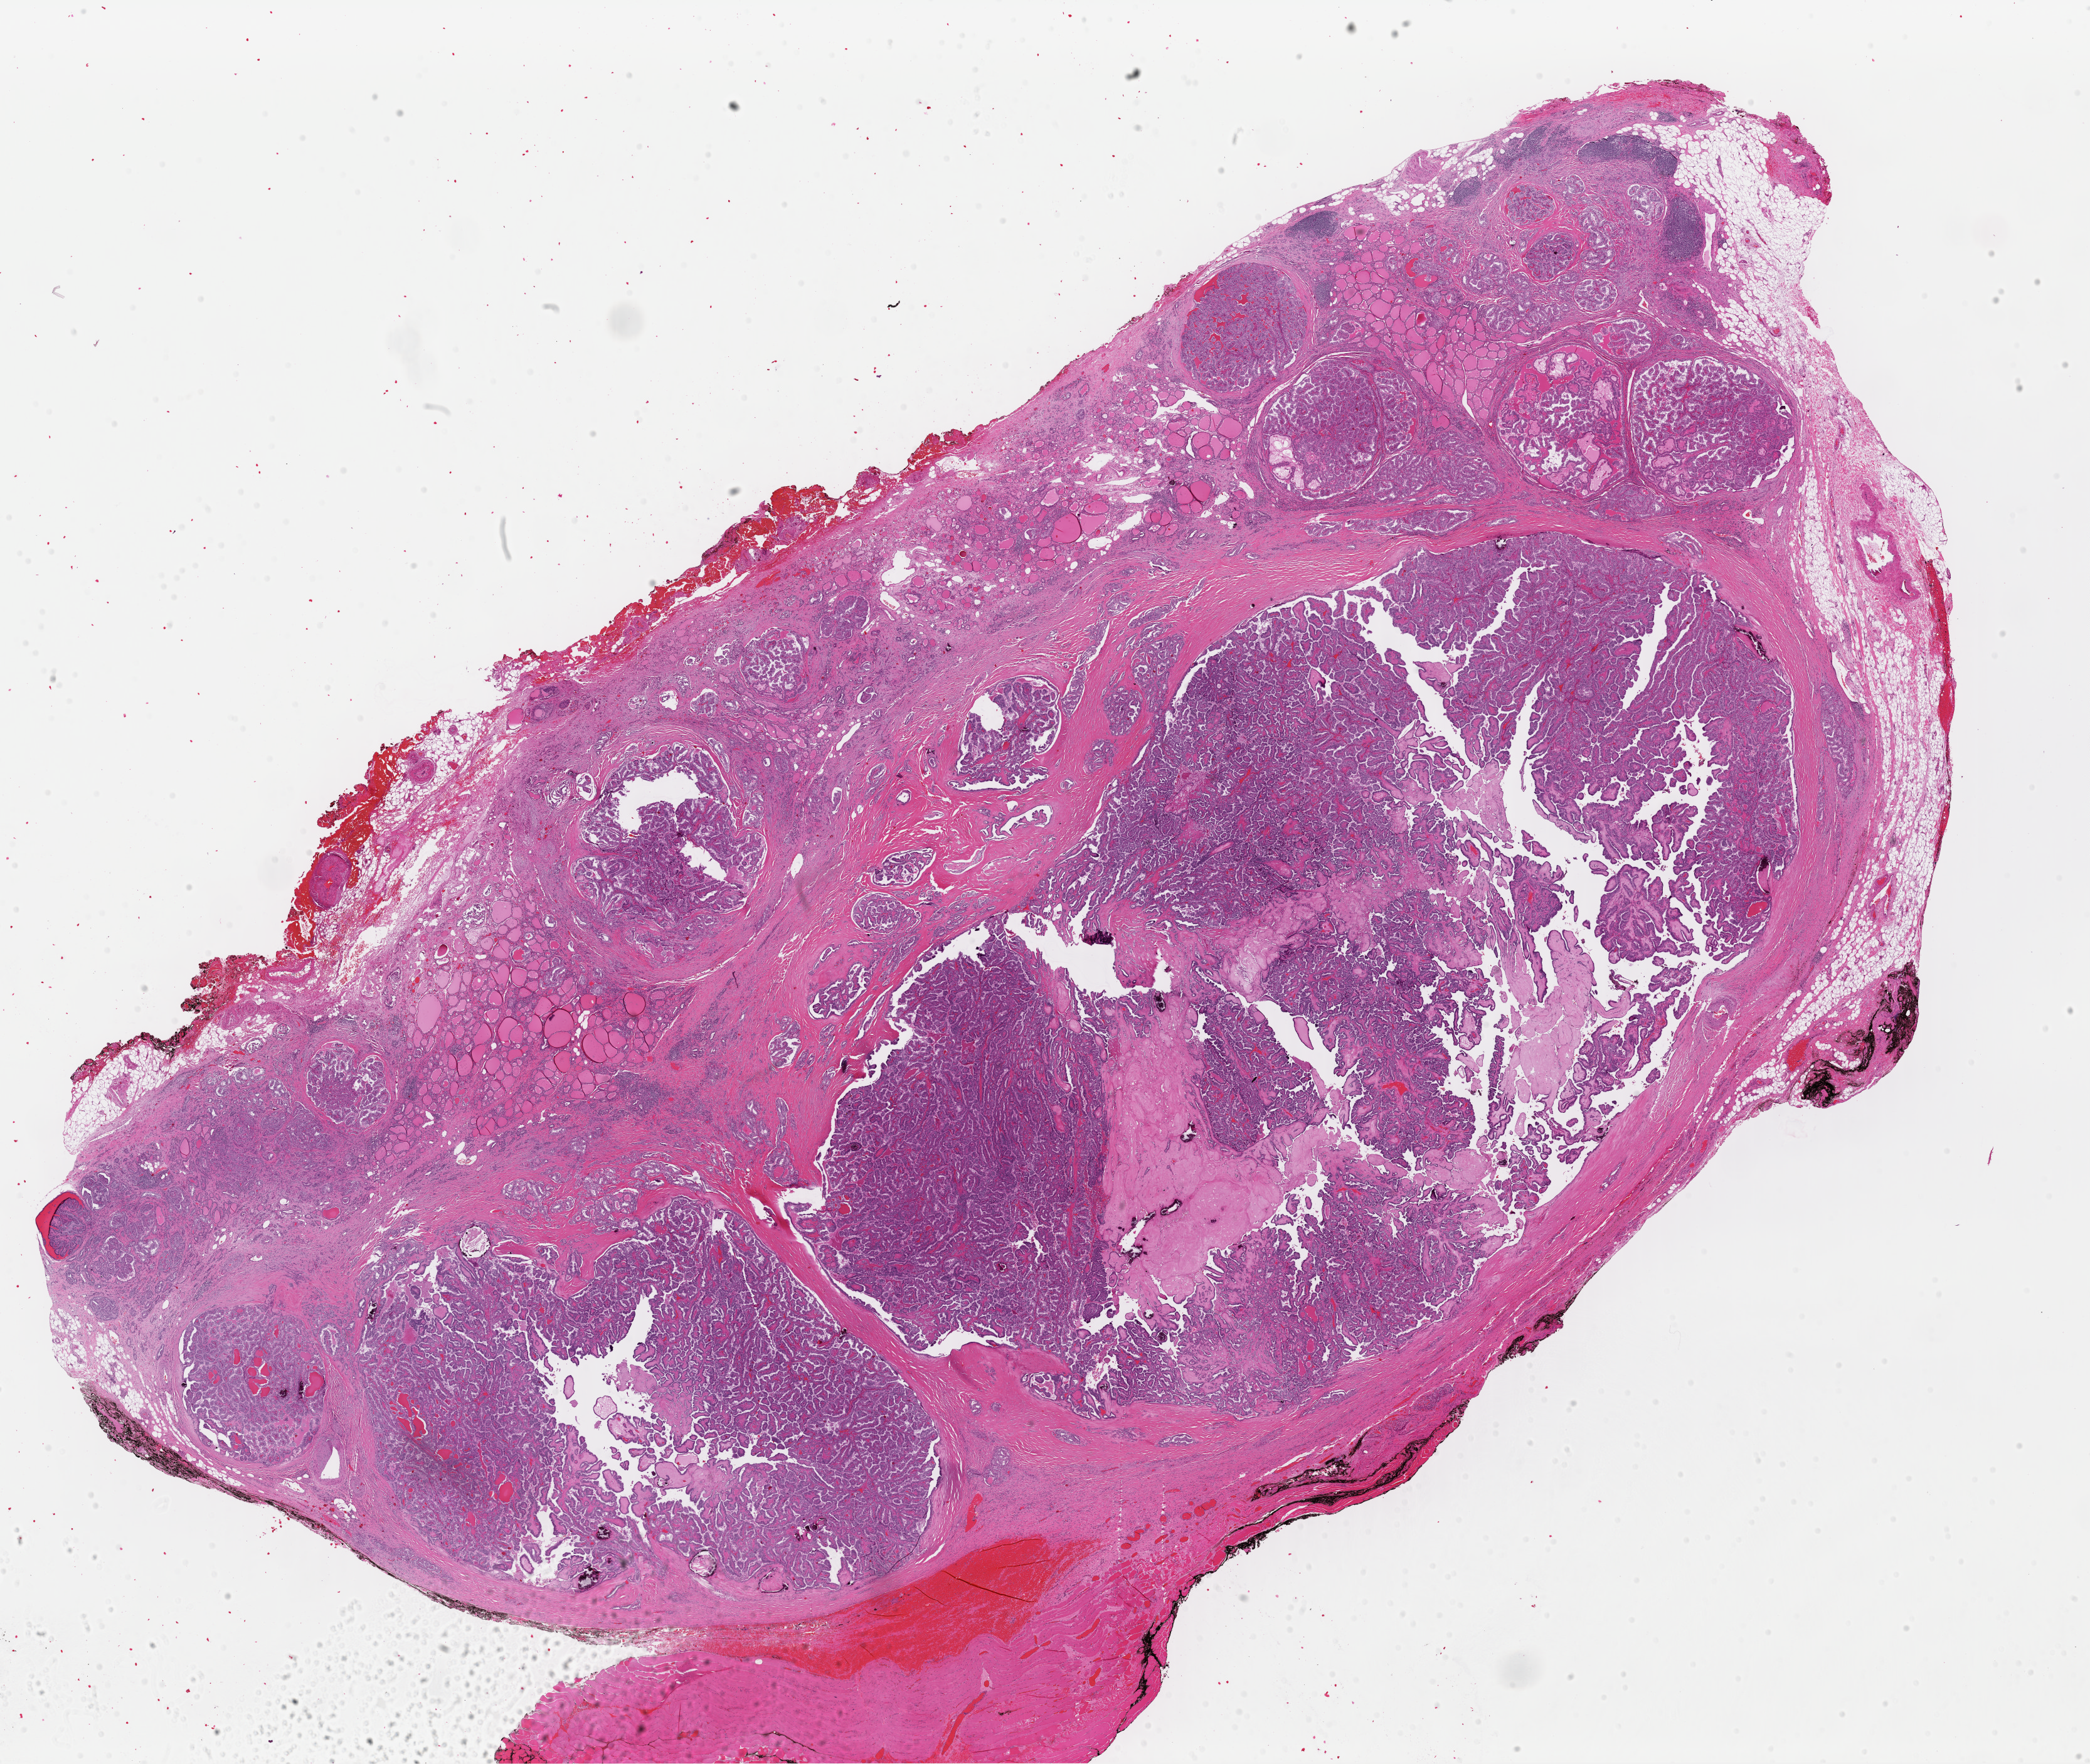
Hematoxylin and eosin (H&E) stained whole-slide image, a low-resolution overview of the entire scanned area, about 26.3 x 22.2 mm, FFPE section, sample: primary tumour, thyroid. Patient: male, age at initial diagnosis 39 years.
• lymph nodes positive (case pathology): 23 of 106 examined
• pathologic diagnosis: Papillary adenocarcinoma, NOS (thyroid gland)
• AJCC pathologic stage: I (7th edition)